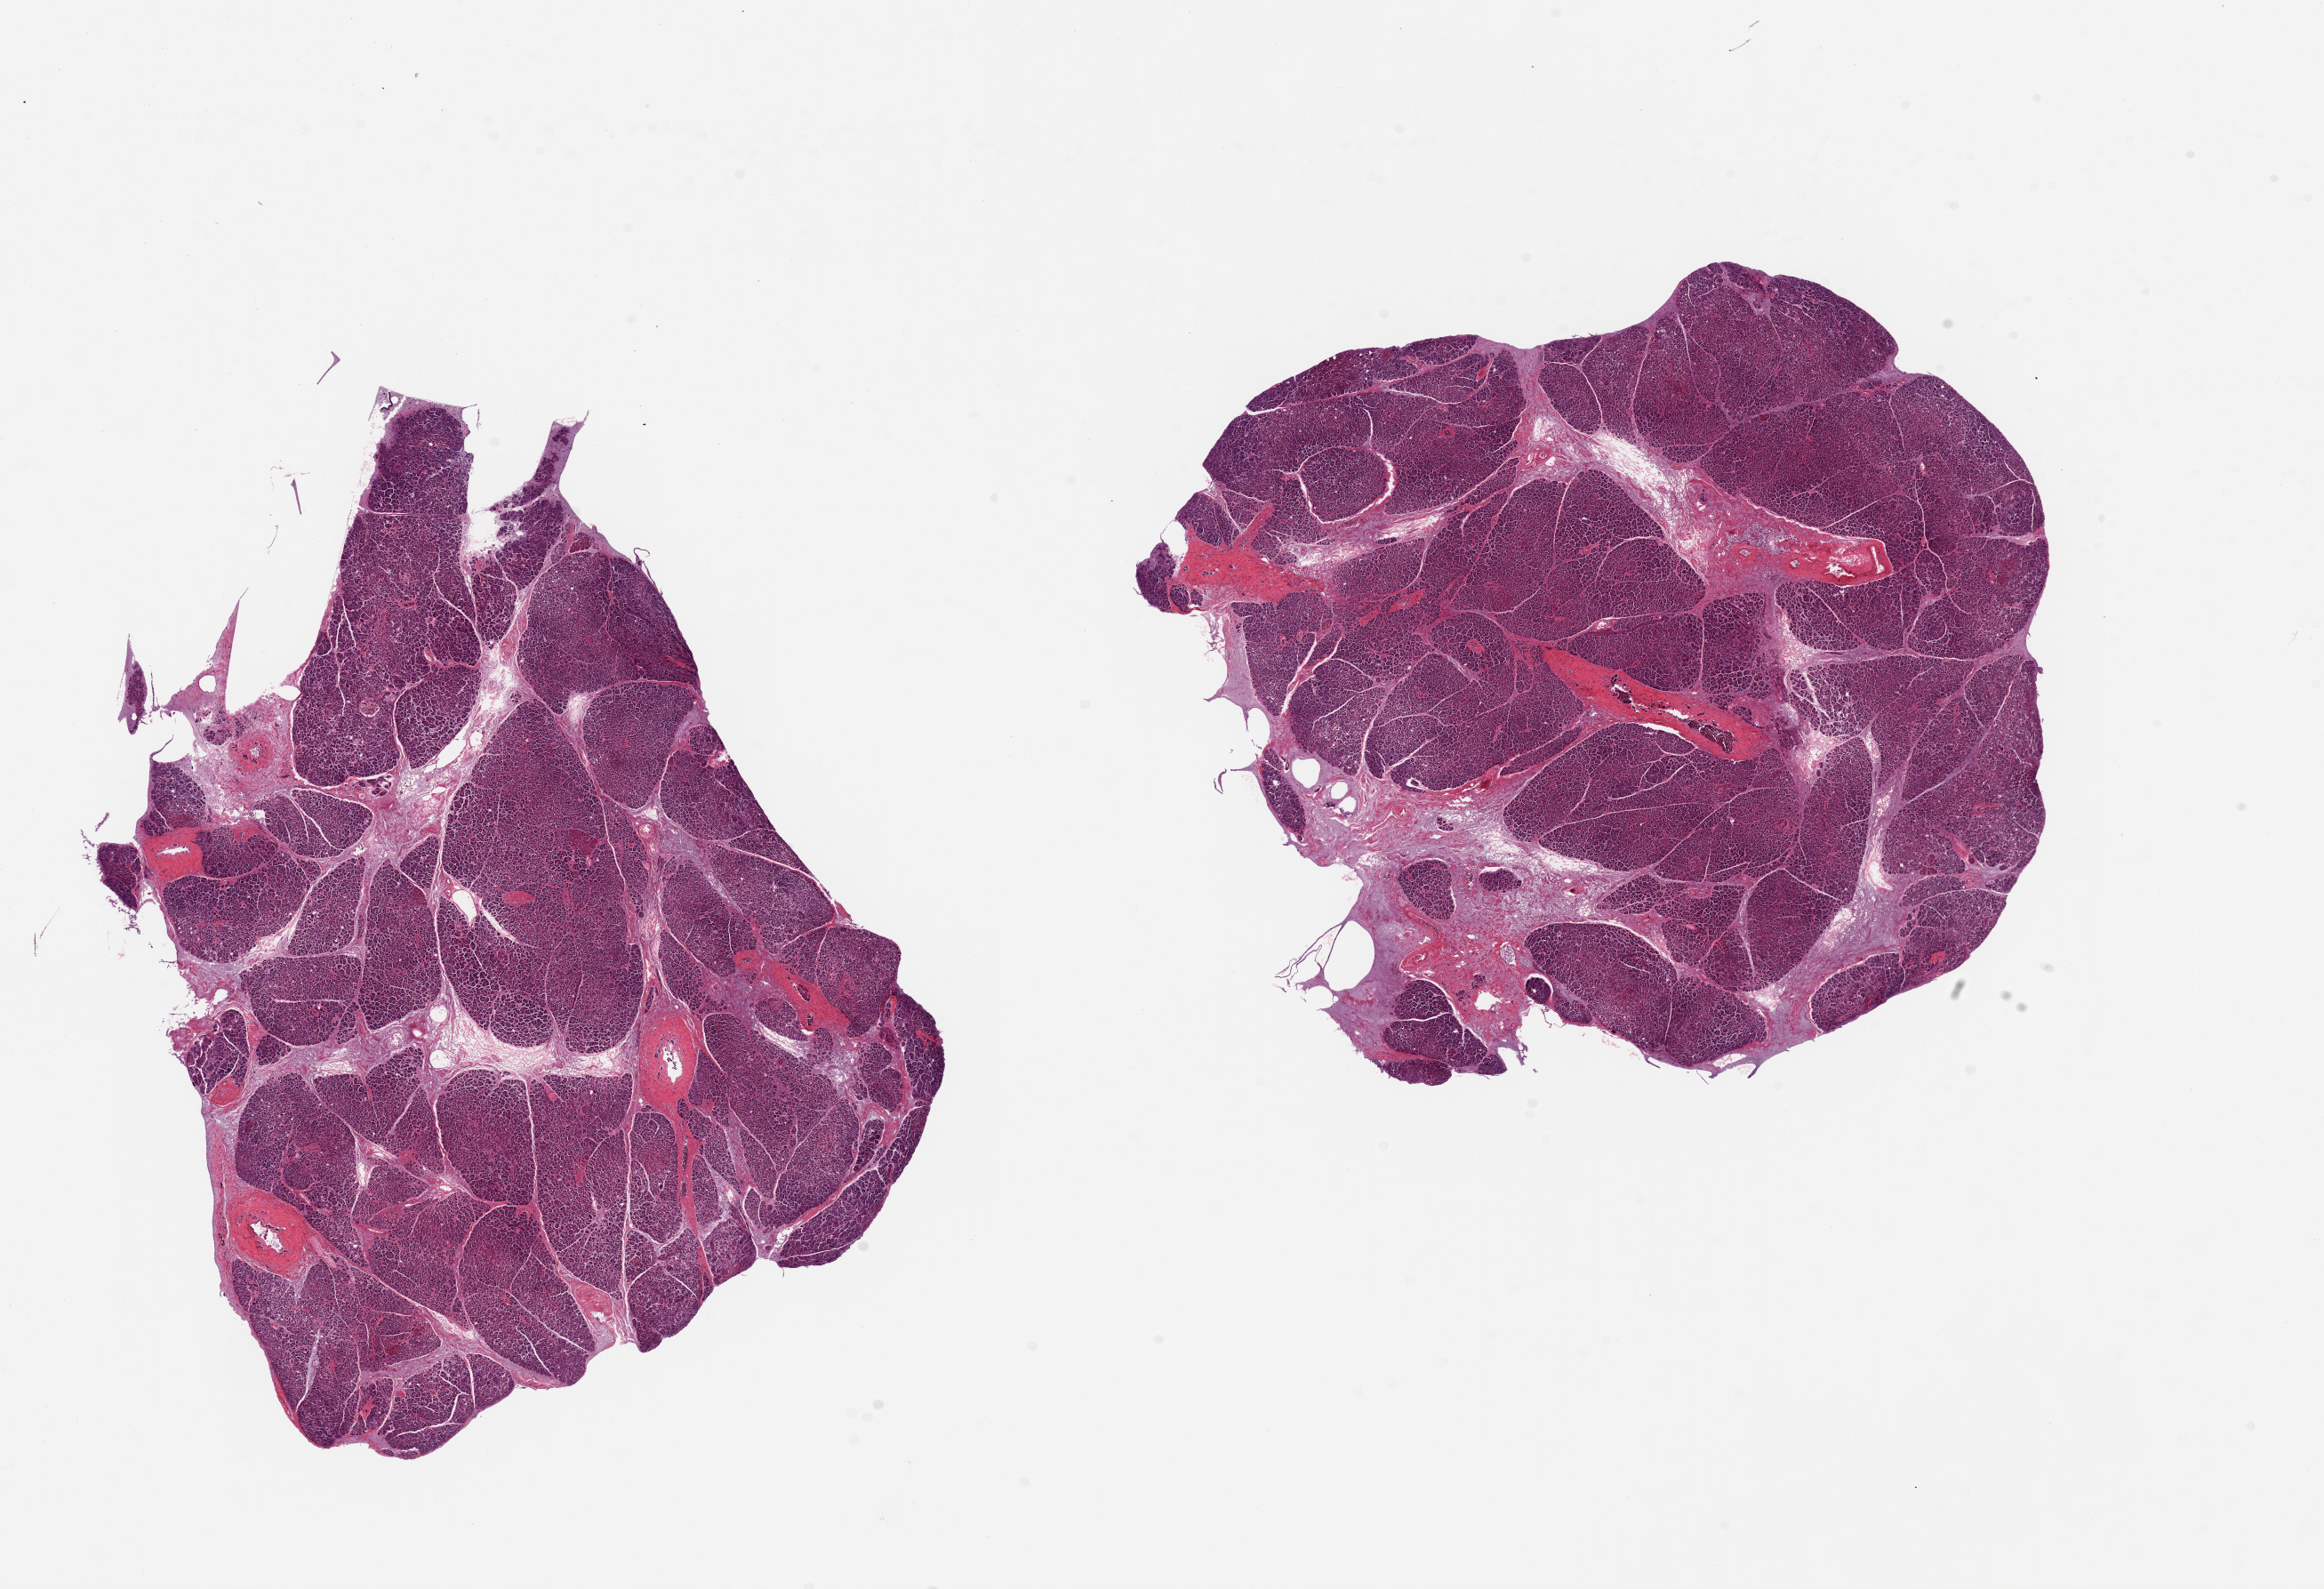
Whole-slide image, H&E stain, brightfield — shown as a low-resolution overview of the whole scanned area (about 20.7 x 14.1 mm); PAXgene-fixed, paraffin-embedded tissue; target tissue: pancreas; donor tissue sample.
* reviewer comment on this tissue sample: 2 pieces ~7x7mm. Minimal fat, moderate saponification. Islets poorly visualized